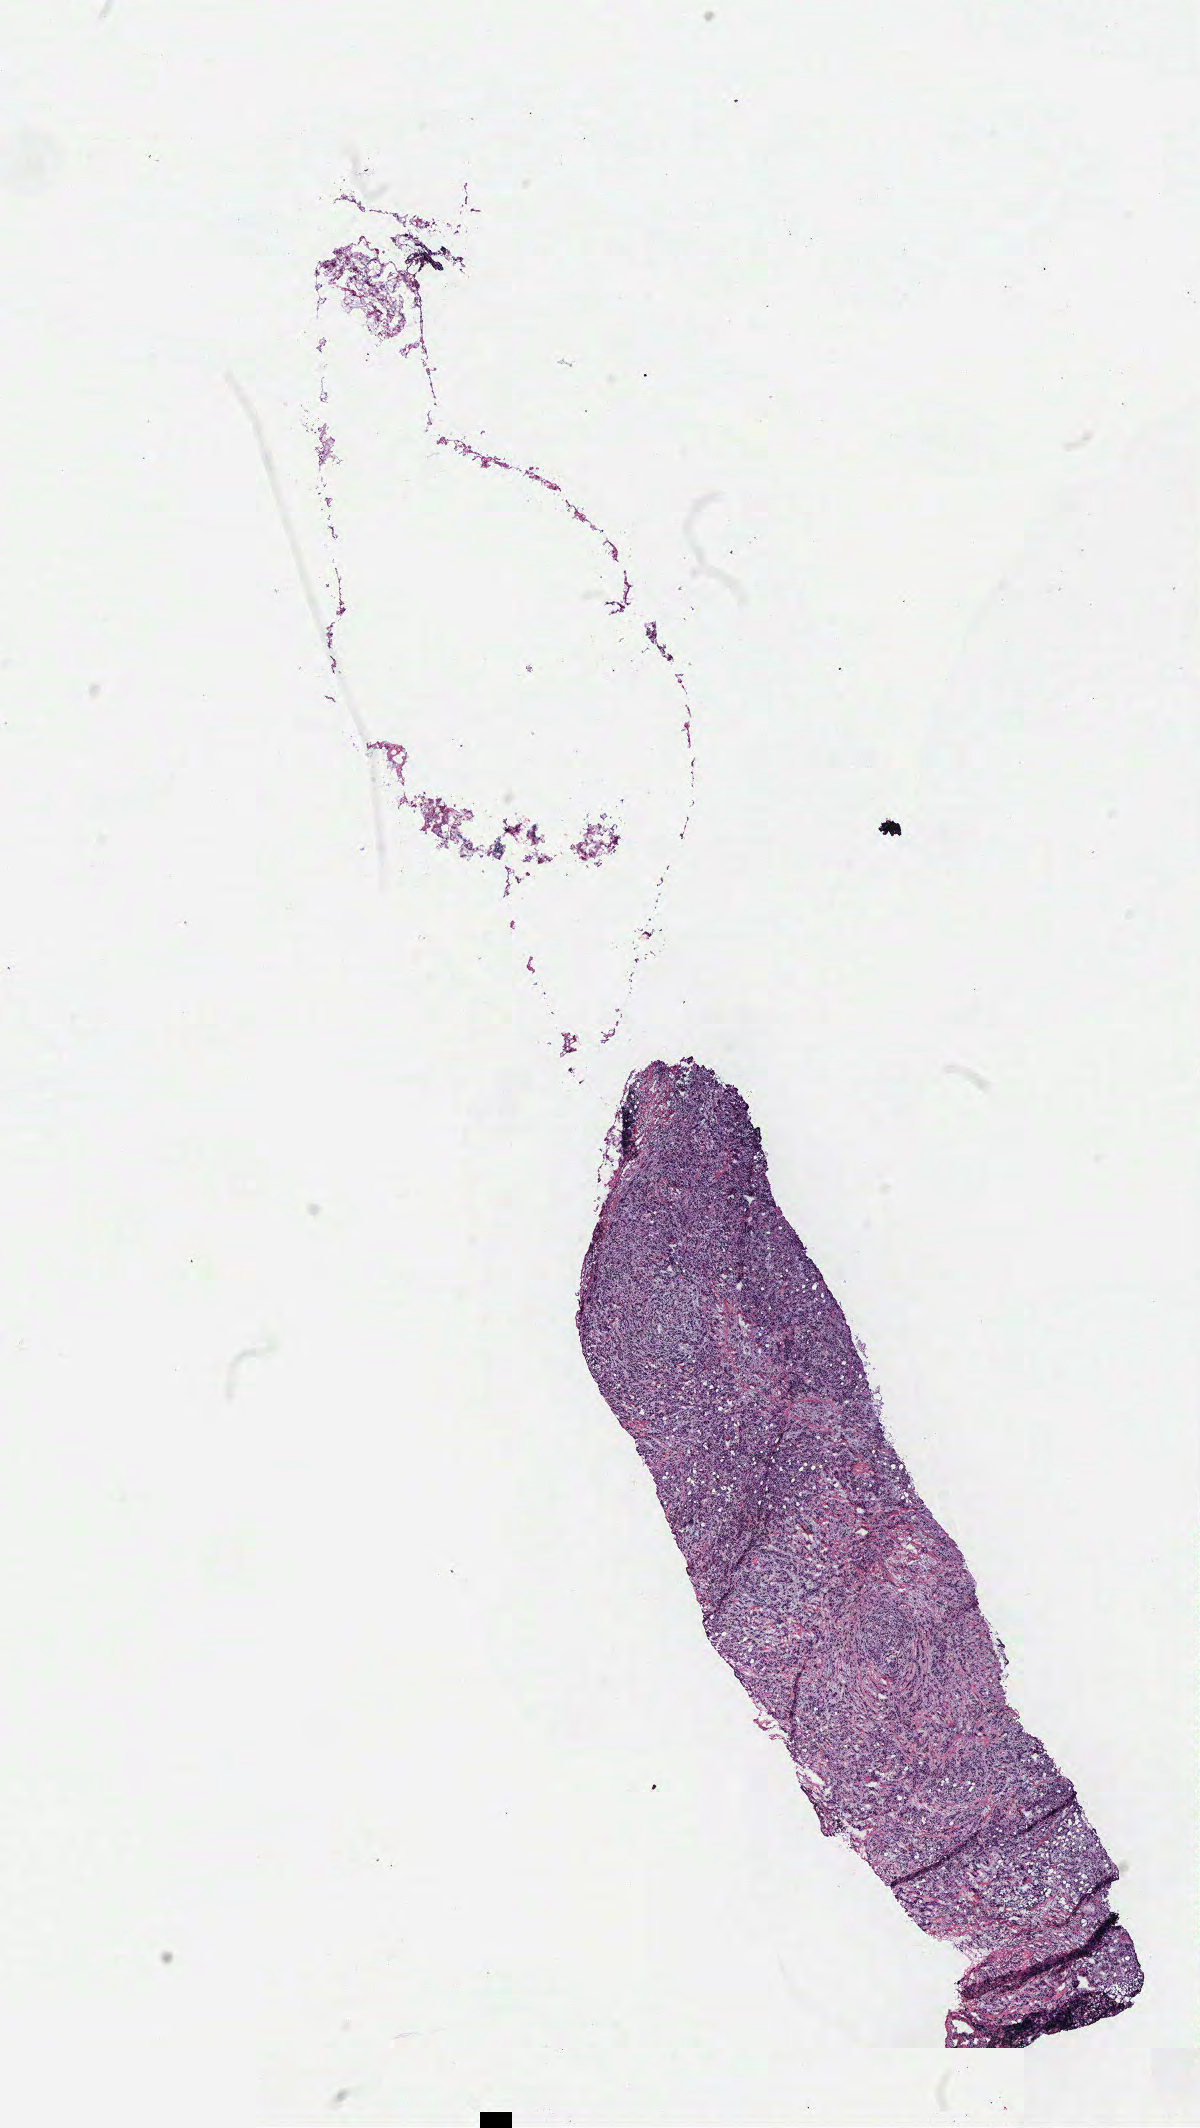
Digitized H&E tissue section (whole slide), shown as a low-resolution overview of the whole scanned area (about 9.6 x 17.0 mm), breast, tissue type not recorded.
* patient diagnosis (cohort enrolment): breast cancer (breast)